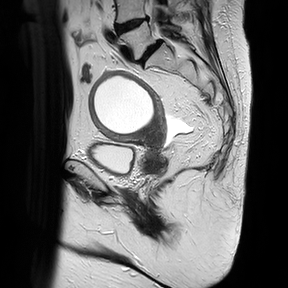
Pelvic MRI for cervical cancer, one sagittal slice. Slice 13 of 30 in the series (ordered by position). T2-weighted. 1.5 T. TE 100 ms, TR 4816.3 ms. 288 × 288 image matrix, field of view 300 × 300 mm. Female patient, age 74 years.
Structures marked on this image (manually delineated by an expert):
- uterus and cervix: box from (x=88, y=69) to (x=170, y=177) px